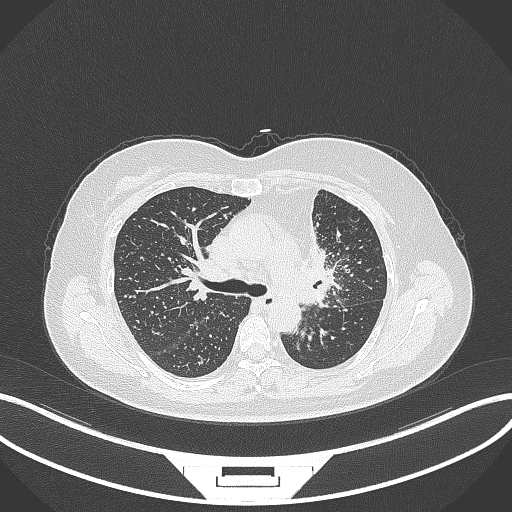
Chest CT, one axial slice. Slice 215 of 348 in the series (ordered by position). Lung window (W 1500 / L -600 HU). 512 × 512 image matrix, field of view 400 × 400 mm. Patient: female, 49 years. Case-level facts recorded for this patient, not image findings: clinical TNM (as recorded): T1c N0 M1.
Structures marked on this image (bounding box drawn by a radiologist):
- lung tumour (recorded histology: adenocarcinoma): box from (x=292, y=243) to (x=336, y=308) px